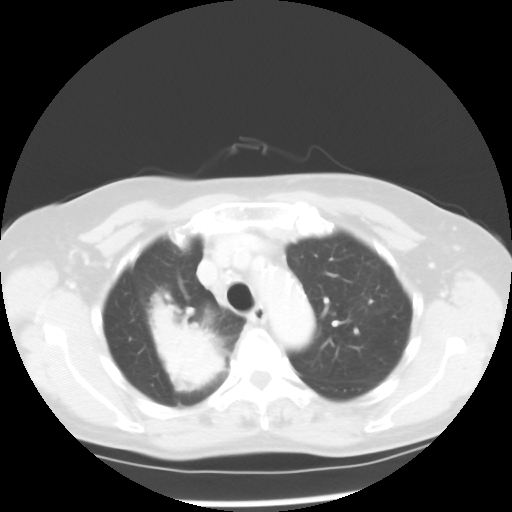
Chest CT, one axial slice; position 39 of 52 along the scan axis; reconstruction kernel STANDARD; lung window (W 1500 / L -600 HU); 512 × 512 image matrix, field of view 328 × 328 mm. Patient: female, 60 years. Case-level facts recorded for this patient, not image findings: clinical TNM (as recorded): T2 N1 M1a.
Annotated regions visible in this slice (bounding box drawn by a radiologist):
- lung tumour (recorded histology: adenocarcinoma): bounding box (x1, y1, x2, y2) in pixels: (145, 290, 228, 397)